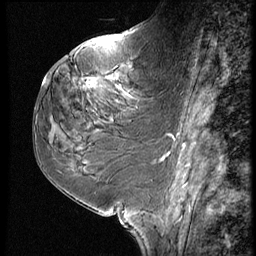
Breast MRI (dynamic contrast-enhanced), one sagittal slice. Slice 31 of 60 in the series (ordered by position). 3 images stored at this slice position (order not interpretable as contrast timing). 1.5 T. TE 4.2 ms, TR 9 ms. 2.5 mm slice thickness. 256 × 256 image matrix. Patient: female, 59 years. From the clinical record (not read from this slice): setting: breast cancer imaged before/during neoadjuvant chemotherapy; receptor status: HER2-positive.
Outlined on this slice (semi-automatically segmented with operator editing):
- analysis volume of interest (the breast-tissue region the enhancement analysis was run in; not a lesion): box from (x=78, y=61) to (x=161, y=125) px
- tumour enhancement mask (voxels above the 140 % enhancement threshold inside the analysis volume of interest): (x=83, y=78)–(x=89, y=80)